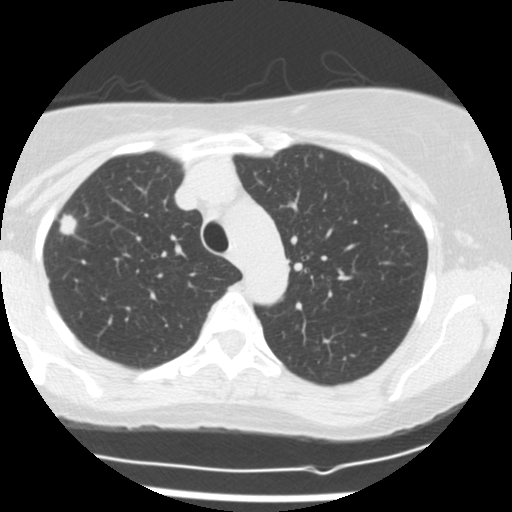
Low-dose screening chest CT, axial slice, baseline screening round, lung window (W 1500 / L -600 HU), 2.5 mm slice thickness, slice 43 of 160 in the series, 512 × 512 image matrix, field of view 300 × 300 mm. Female participant, aged 58 years at enrolment.
Expert reader's lesion annotation, box from (x=43, y=204) to (x=91, y=241) px. The exam's reader record, not a measurement of the box and not confirmed to be the same lesion: non-calcified nodule or mass ≥4 mm, right upper lobe, 12 × 9 mm, spiculated (stellate) margins, soft tissue attenuation. Participant outcome: lung cancer diagnosed 21 days after this screen — adenocarcinoma, NOS, right upper lobe, moderately differentiated (G2), stage IA (AJCC 6th edition), 10 mm at pathology.